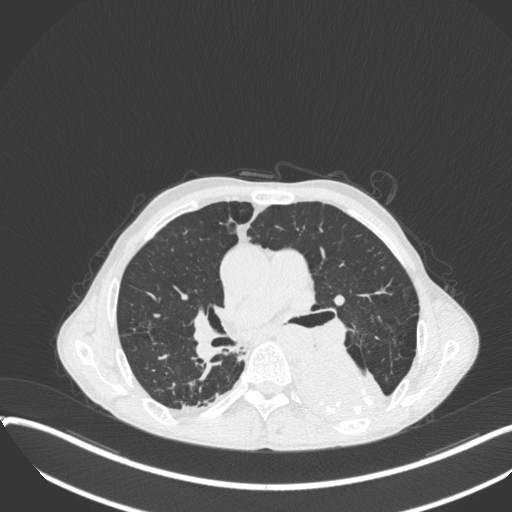
Chest CT, one axial slice; slice 216 of 400 in the series (ordered by position); 120 kVp; lung window (W 1500 / L -600 HU); 1 mm slice thickness; 512 × 512 image matrix. Patient: male, 57 years. Case-level facts recorded for this patient, not image findings: clinical TNM (as recorded): T4 N0 M0.
Outlined on this slice (rectangle marked by the reading radiologist):
- lung tumour (recorded histology: squamous cell carcinoma): box from (x=289, y=345) to (x=394, y=428) px